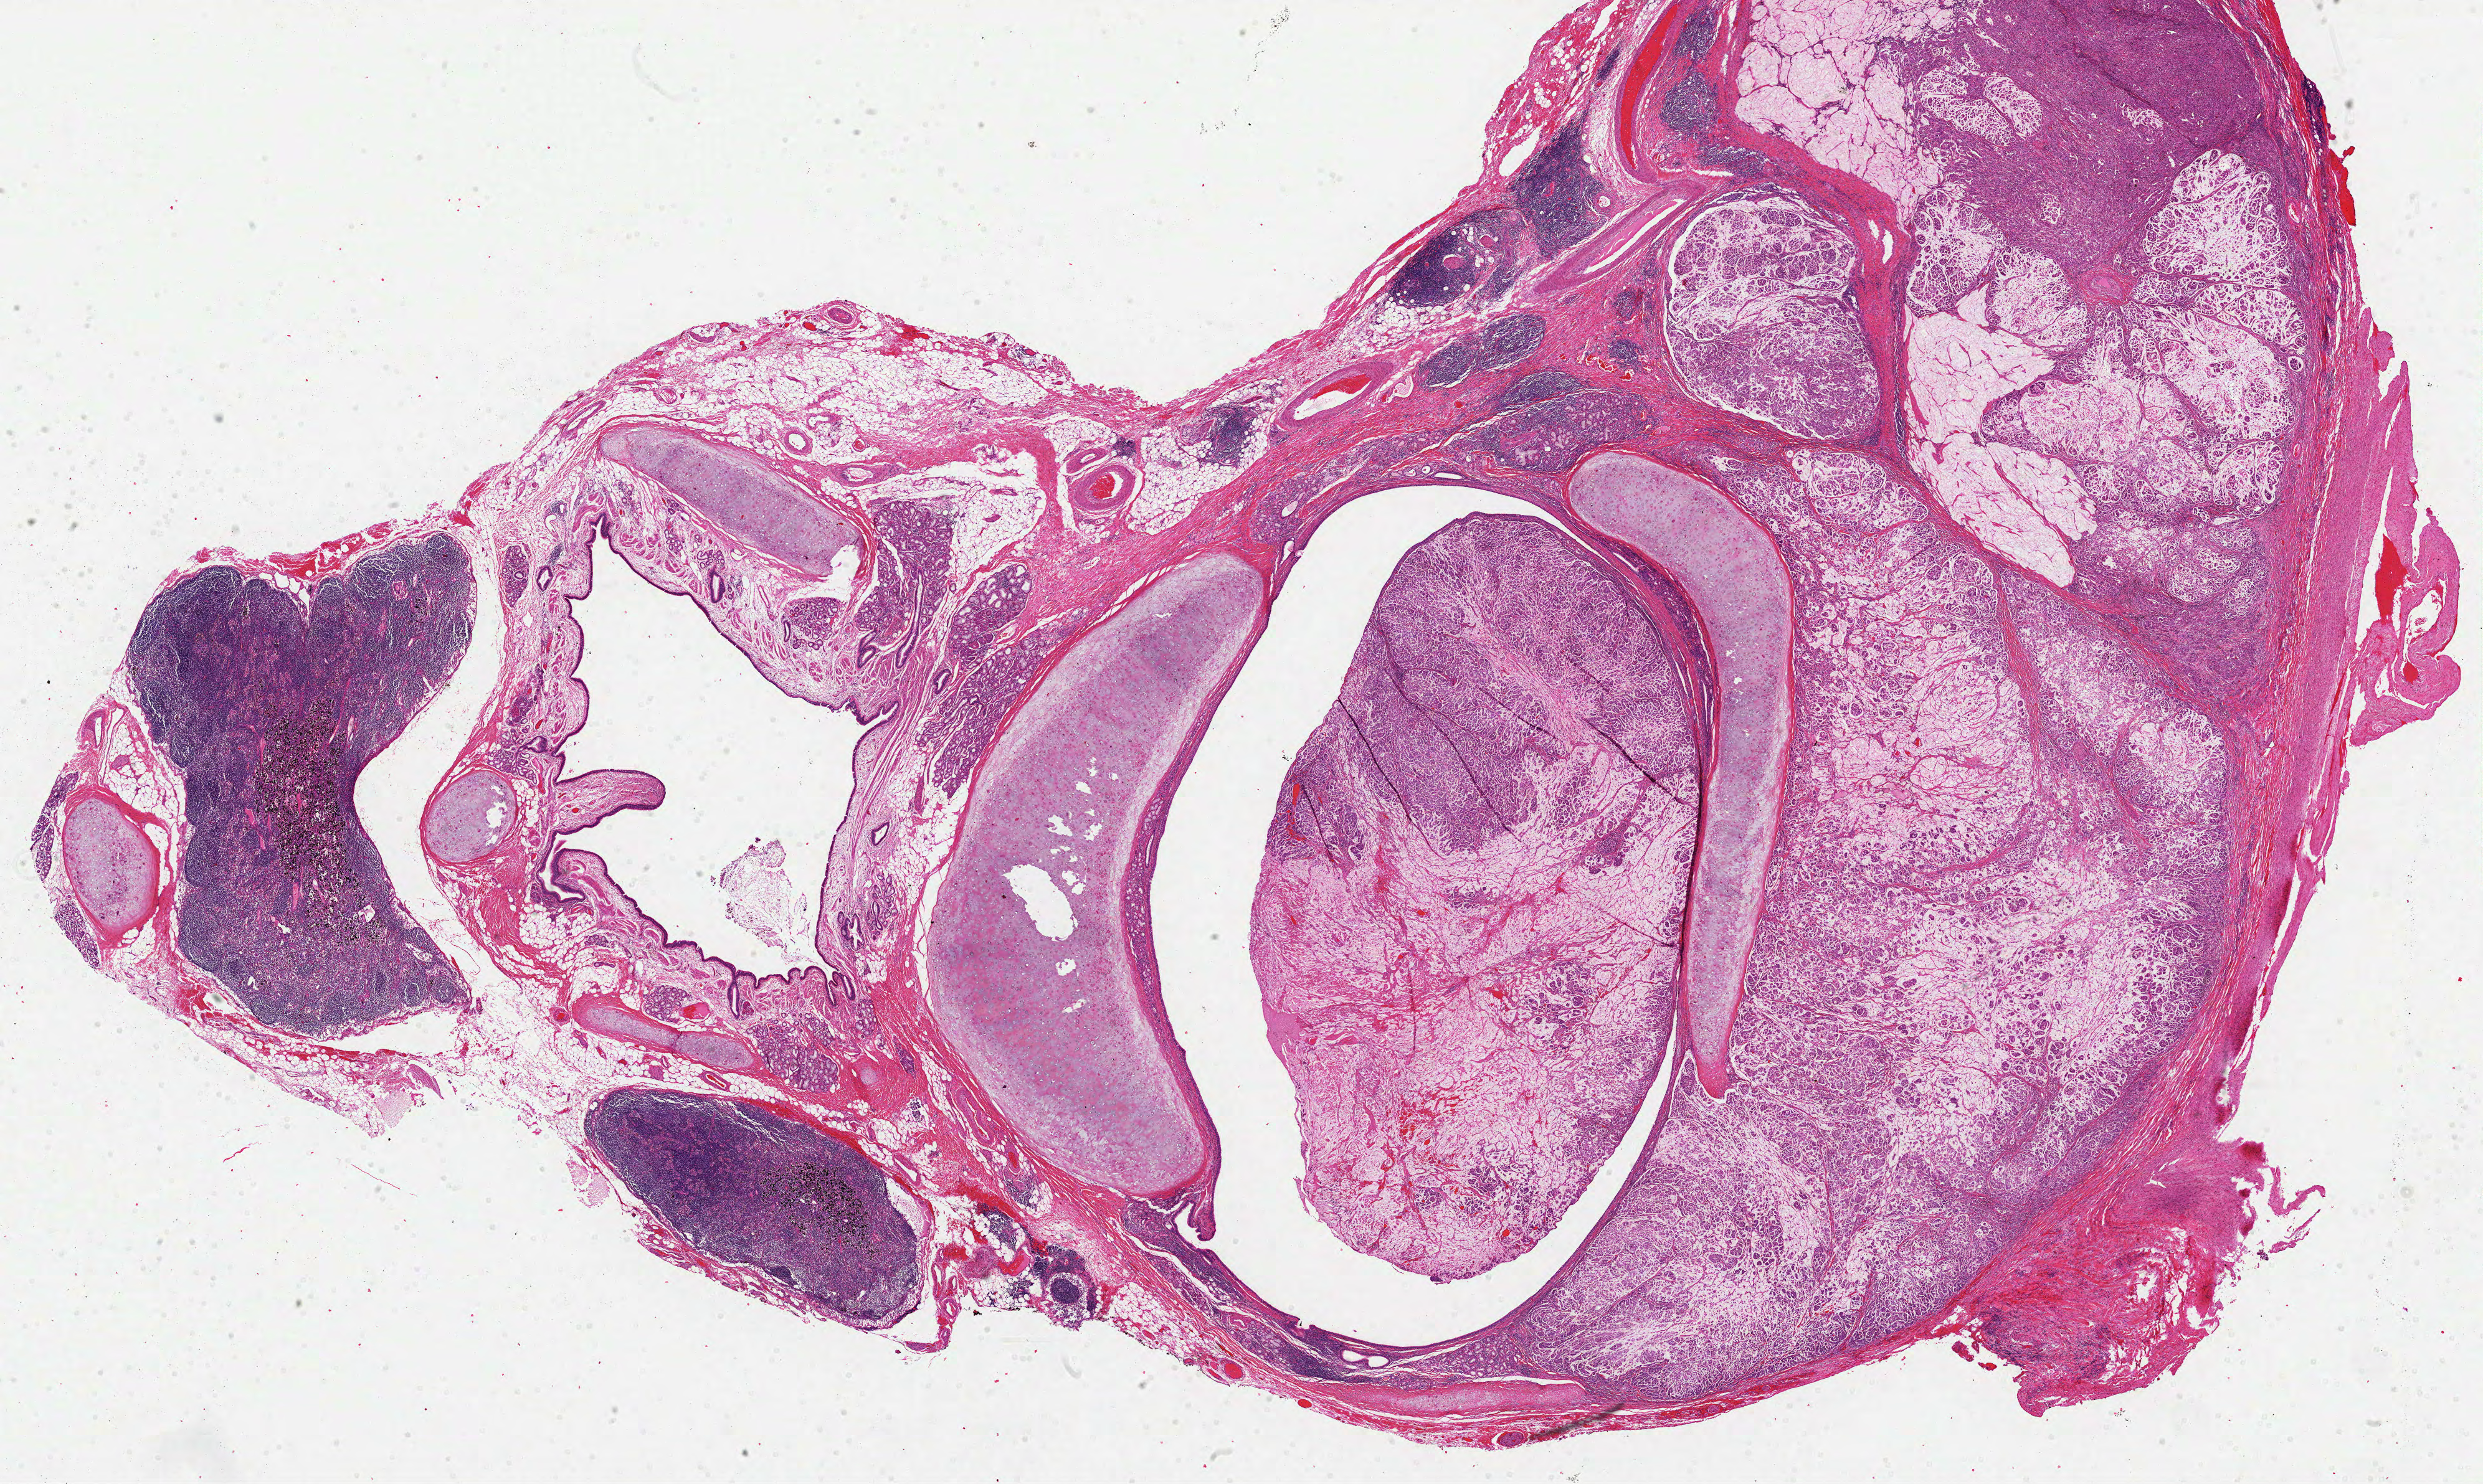
Hematoxylin and eosin (H&E) stained whole-slide image — shown as a low-resolution overview of the whole scanned area (about 32.1 x 19.2 mm); formalin-fixed paraffin-embedded (FFPE) diagnostic section; sample: primary tumour, lung. Patient: female, age at initial diagnosis 68 years.
- histologic diagnosis: Adenocarcinoma, NOS (upper lobe, lung)
- AJCC pathologic stage: IIB (4th edition)